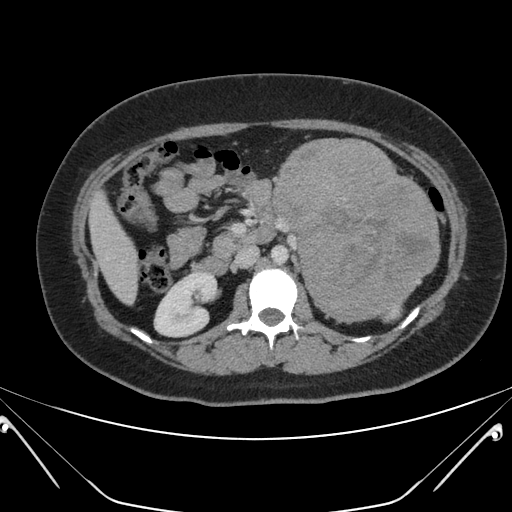
Contrast-enhanced abdominal CT, one axial slice. Slice 110 of 168 in the series (ordered by position). 120 kVp. Soft-tissue window (W 400 / L 40 HU). 3 mm slice thickness. 512 × 512 image matrix. Female patient, age 26 years. From the clinical record (not read from this slice): diagnosis: adrenocortical carcinoma; tumour side: left adrenal; tumour size at pathology: 28 cm; Ki-67 index: 20 %; stage (as recorded): 2.
Structures marked on this image (semi-automatic segmentation, software-assisted and operator-edited):
- mass: bounding box [x1, y1, x2, y2] px = [273, 137, 439, 321]